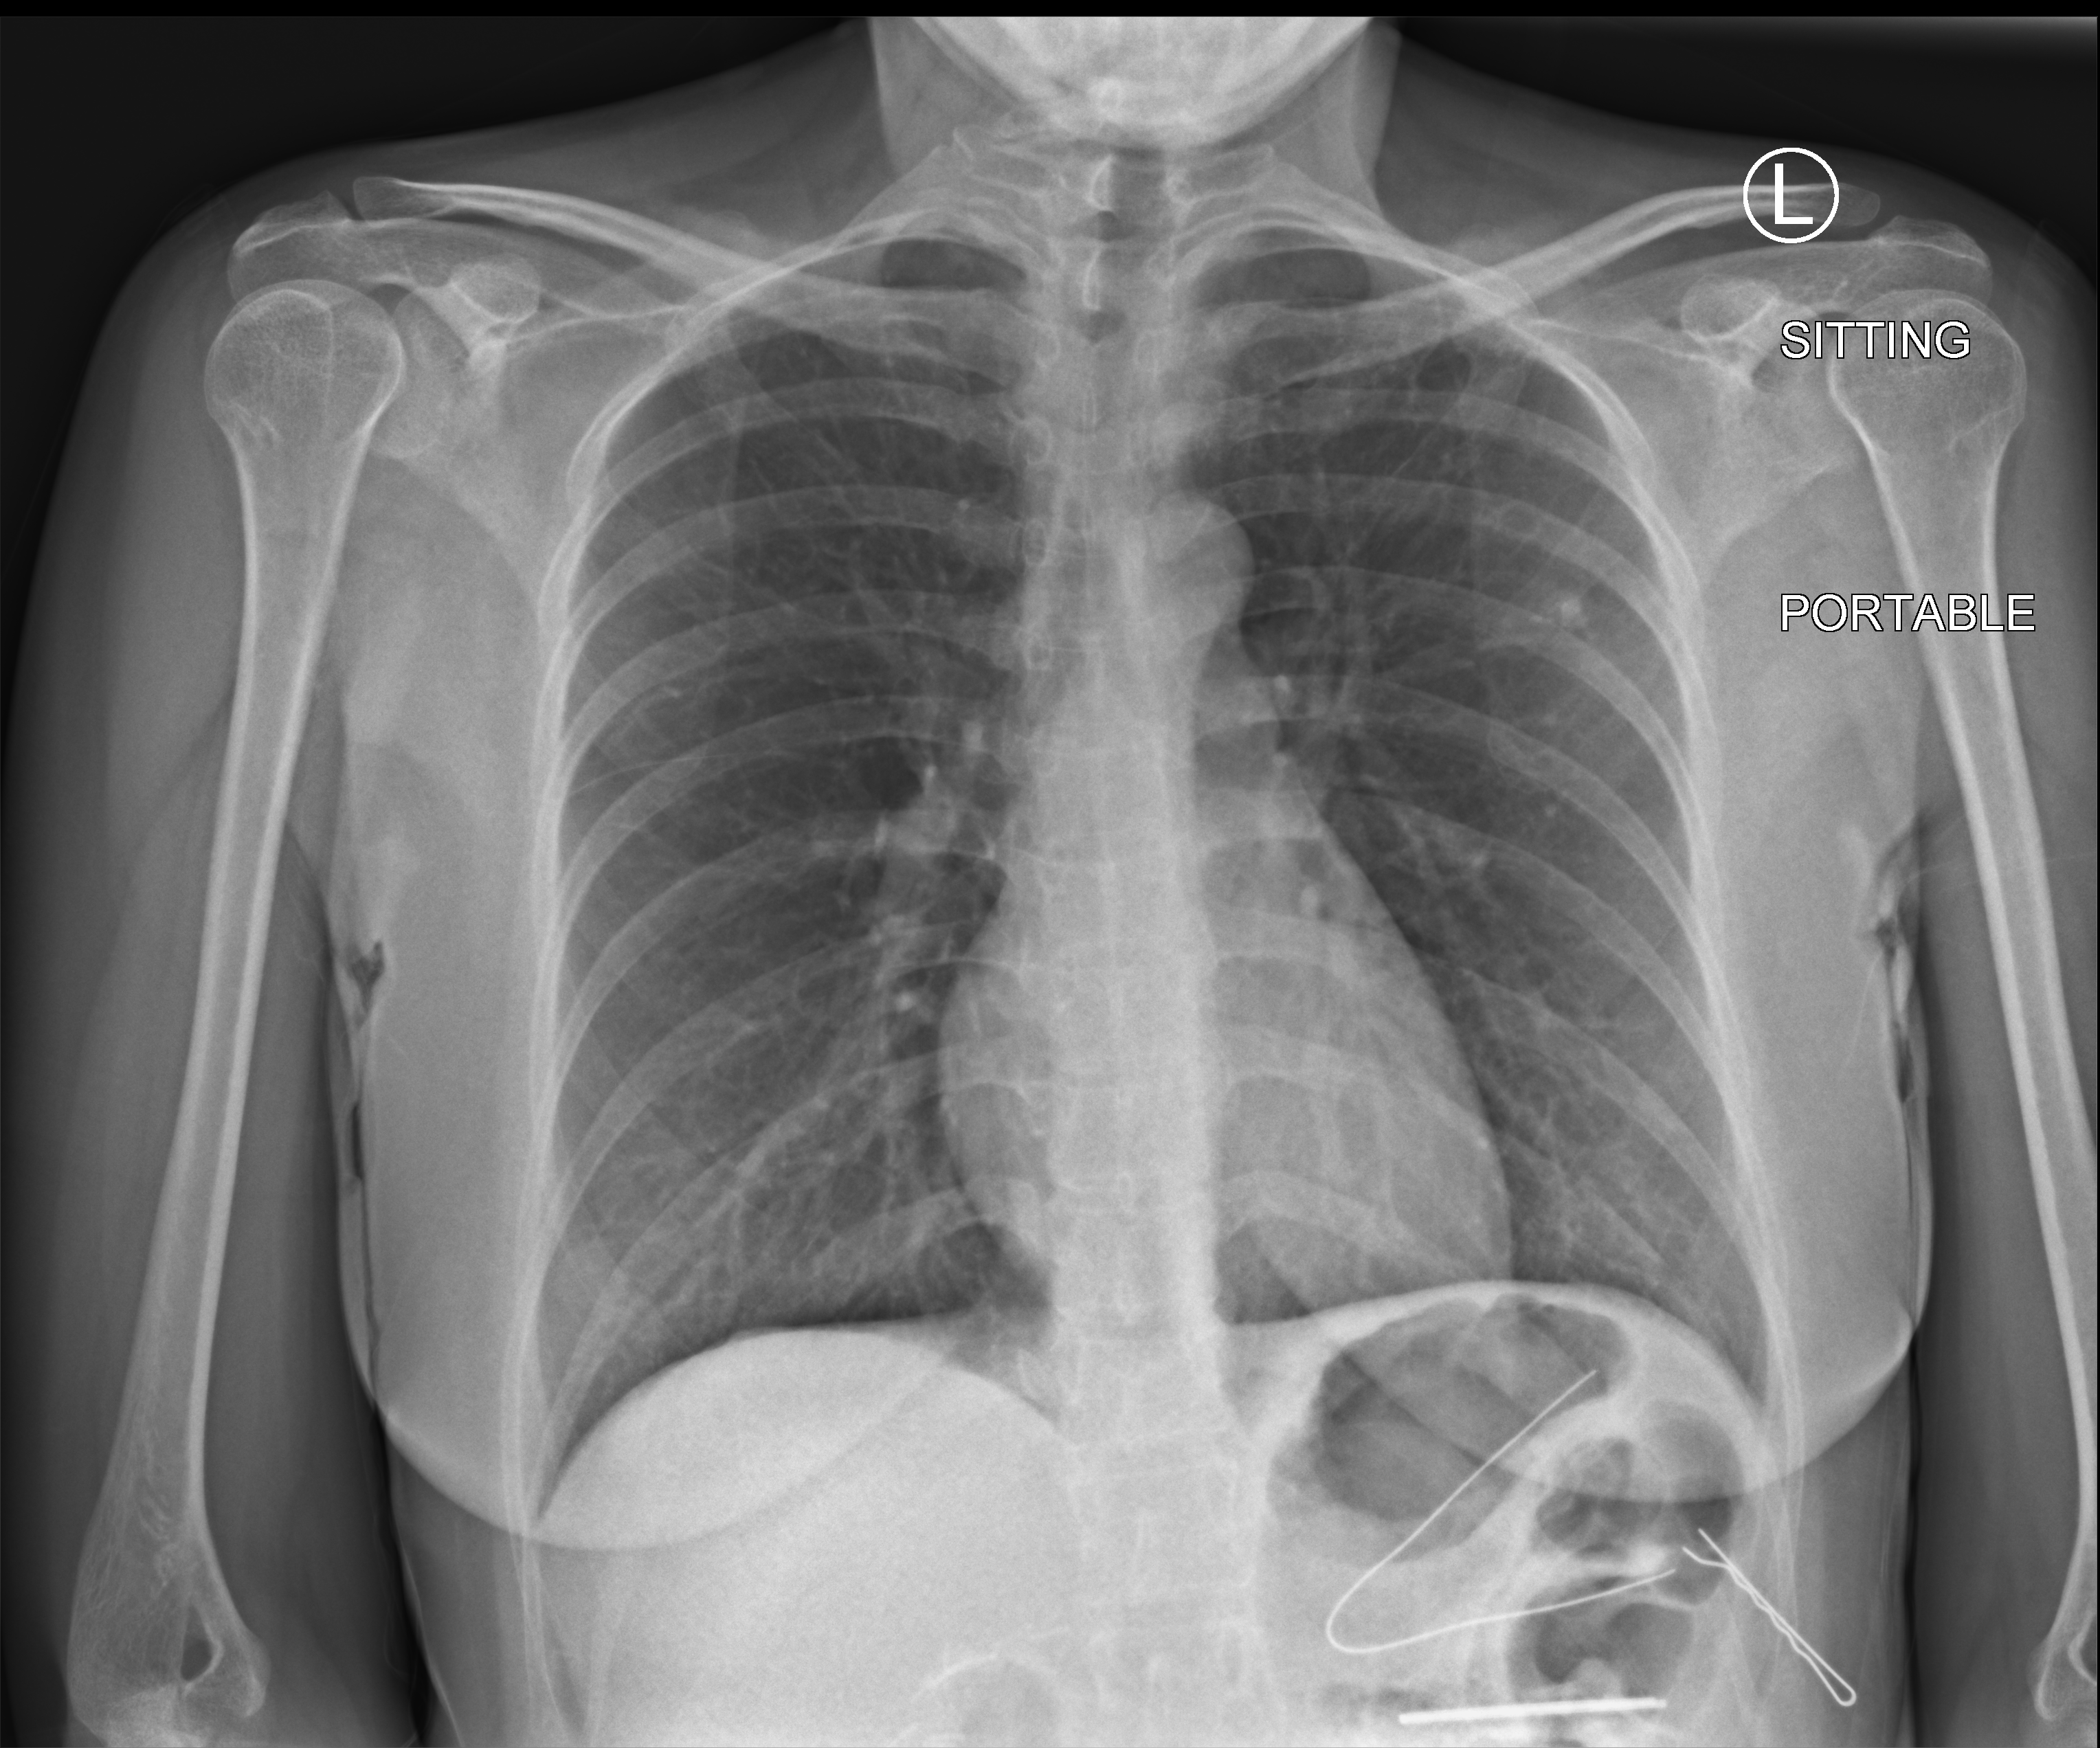
Bedside chest radiograph (computed radiography); anteroposterior (AP) projection. Patient hospitalised with COVID-19; female, aged 18–59 years.
Admission-level facts for this patient (not findings on this image; timing relative to this image not recorded): admitted to intensive care during this hospital stay: no; hypertension (admission record): no; COPD (admission record): no.